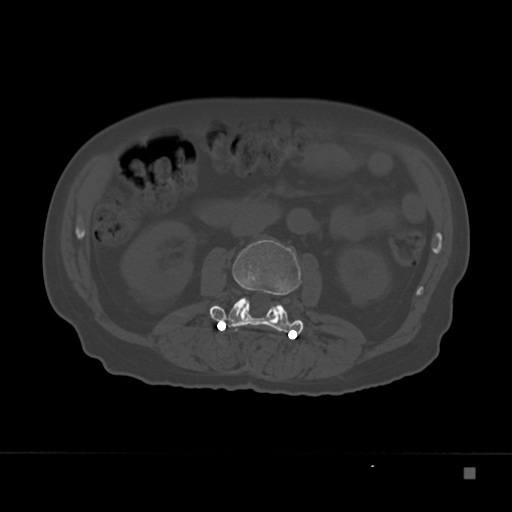
CT including the spine, one axial slice; position 83 of 332 along the scan axis; reconstruction kernel Br40s; bone window (W 1800 / L 400 HU); 1.5 mm slice thickness; 512 × 512 image matrix. Patient: male, 72 years. Case-level facts recorded for this patient, not image findings: primary cancer: skeletal.
Outlined on this slice (semi-automatic segmentation, software-assisted and operator-edited):
- L2 vertebra: box from (x=211, y=240) to (x=302, y=334) px
- L3 vertebra: (x=210, y=297)–(x=303, y=334)